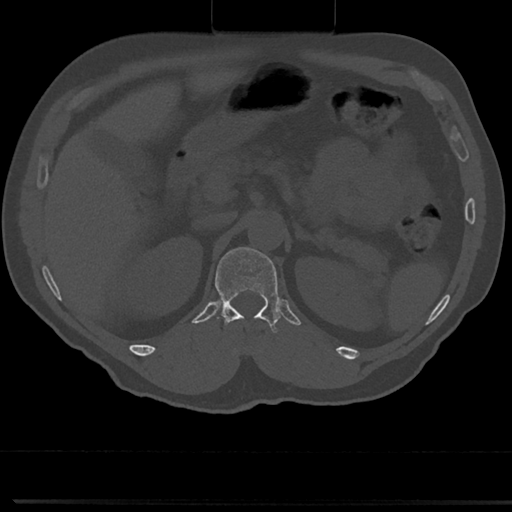
CT including the spine, one axial slice. Position 144 of 817 along the scan axis. Reconstruction kernel Br40s/3. 120 kVp. Bone window (W 1800 / L 400 HU). 0.5 mm slice thickness. 512 × 512 image matrix. Male patient, age 61 years. From the clinical record (not read from this slice): primary cancer: prostate.
Structures marked on this image (semi-automatic segmentation, software-assisted and operator-edited):
- T12 vertebra: bounding box (x1, y1, x2, y2) in pixels: (211, 247, 281, 354)